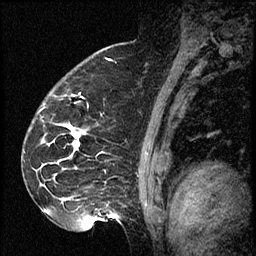
Breast MRI (dynamic contrast-enhanced), one sagittal slice. Position 47 of 60 along the scan axis. Dynamic contrast-enhanced series, image 2 of 2 at this slice position (ordered by acquisition). 1.5 T. TE 4.2 ms, TR 17.3 ms. 2 mm slice thickness. 256 × 256 image matrix, field of view 200 × 200 mm. Female patient. Case-level facts recorded for this patient, not image findings: setting: breast cancer imaged before/during neoadjuvant chemotherapy; receptor status: HR-positive, HER2-negative.
Annotated regions visible in this slice (semi-automatically segmented with operator editing):
- analysis volume of interest (the breast-tissue region the enhancement analysis was run in; not a lesion): bounding box [x1, y1, x2, y2] px = [41, 93, 115, 223]
- tumour enhancement mask (voxels above the 100 % enhancement threshold inside the analysis volume of interest): [73, 131, 79, 150]